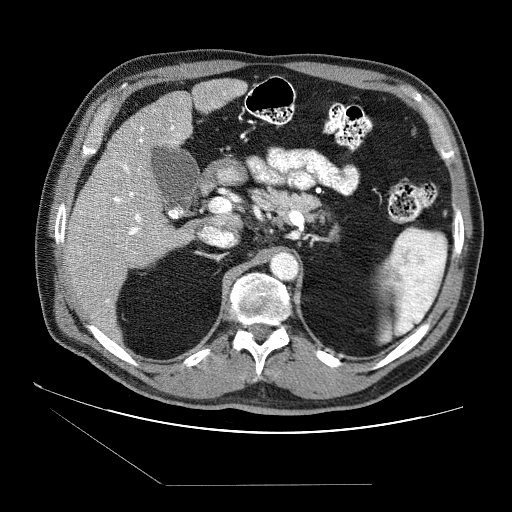
Contrast-enhanced abdominal CT (liver protocol), one axial slice; slice 41 of 87 in the series (ordered by position); reconstruction kernel STANDARD; soft-tissue window (W 400 / L 40 HU); 512 × 512 image matrix, field of view 400 × 400 mm. Case-level facts recorded for this patient, not image findings: diagnosis: hepatocellular carcinoma (patient treated with transarterial chemoembolisation; whether this scan precedes or follows treatment is not stated here); TNM stage (as recorded): Stage-II; Child-Pugh class: B; tumour nodularity: multinodular; tumour size: 2.6 cm.
Annotated regions visible in this slice (semi-automatic segmentation, software-assisted and operator-edited):
- liver parenchyma outside the tumour (the mass and vessels are separate outlines, so this box may not span the whole liver): bounding box (x1, y1, x2, y2) in pixels: (64, 78, 246, 330)
- liver vessels: (79, 92, 226, 302)